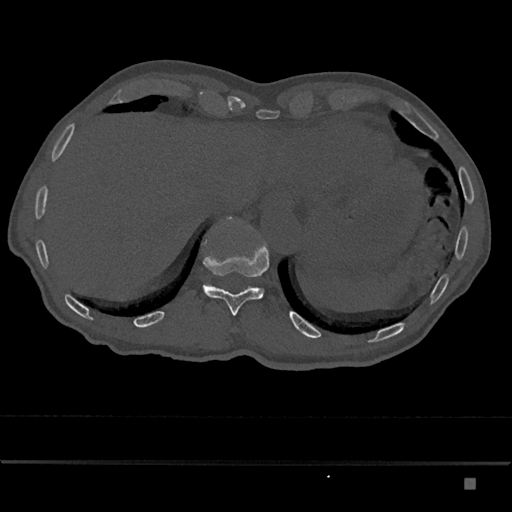
CT including the spine, one axial slice. Position 670 of 797 along the scan axis. Reconstruction kernel Br40s/3. 120 kVp. Bone window (W 1800 / L 400 HU). 0.5 mm slice thickness. 512 × 512 image matrix, field of view 390 × 390 mm. Male patient, age 72 years. Case-level facts recorded for this patient, not image findings: primary cancer: prostate.
Annotated regions visible in this slice (semi-automatic segmentation, software-assisted and operator-edited):
- T11 vertebra: bounding box (x1, y1, x2, y2) in pixels: (203, 217, 270, 316)
- T12 vertebra: (228, 217, 240, 222)